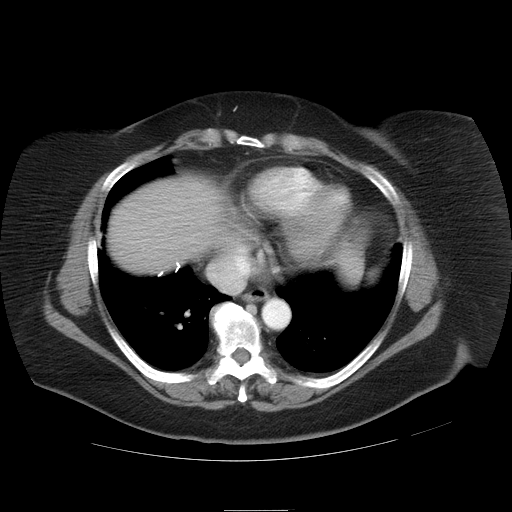
Contrast-enhanced abdominal CT, one axial slice. Slice 34 of 37 in the series (ordered by position). Reconstruction kernel STANDARD. 120 kVp. Intravenous contrast given. Soft-tissue window (W 400 / L 40 HU). 7.5 mm slice thickness. 512 × 512 image matrix, field of view 422 × 422 mm. Female patient, age 68 years. From the clinical record (not read from this slice): diagnosis: colorectal cancer liver metastases, imaged before liver resection.
Outlined on this slice (expert manual segmentation):
- liver: bounding box <108,176,234,273> (left, top, right, bottom; pixels)
- planned liver remnant (the part of the liver to remain after resection): <107,176,234,273>